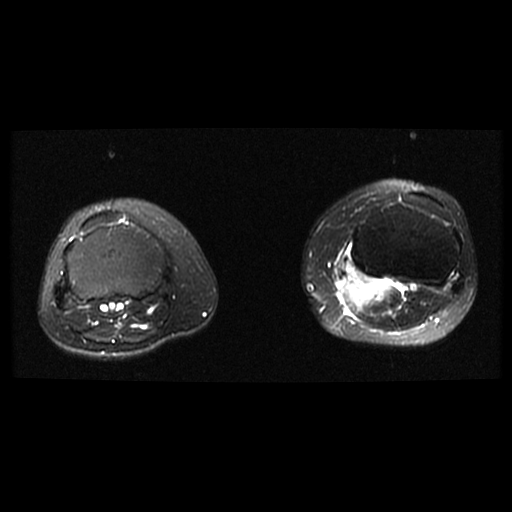
MRI of an extremity soft-tissue mass, one axial slice; position 25 of 38 along the scan axis; T2-weighted fat-saturated; 6 mm slice thickness; 512 × 512 image matrix, field of view 330 × 330 mm. Female patient. From the clinical record (not read from this slice): histological type: extraskeletal high grade osteogenic sarcoma; grade: high; site of the primary tumour: left calf.
Outlined on this slice (manually delineated by an expert):
- gross tumour volume (mass): box from (x=346, y=276) to (x=389, y=307) px